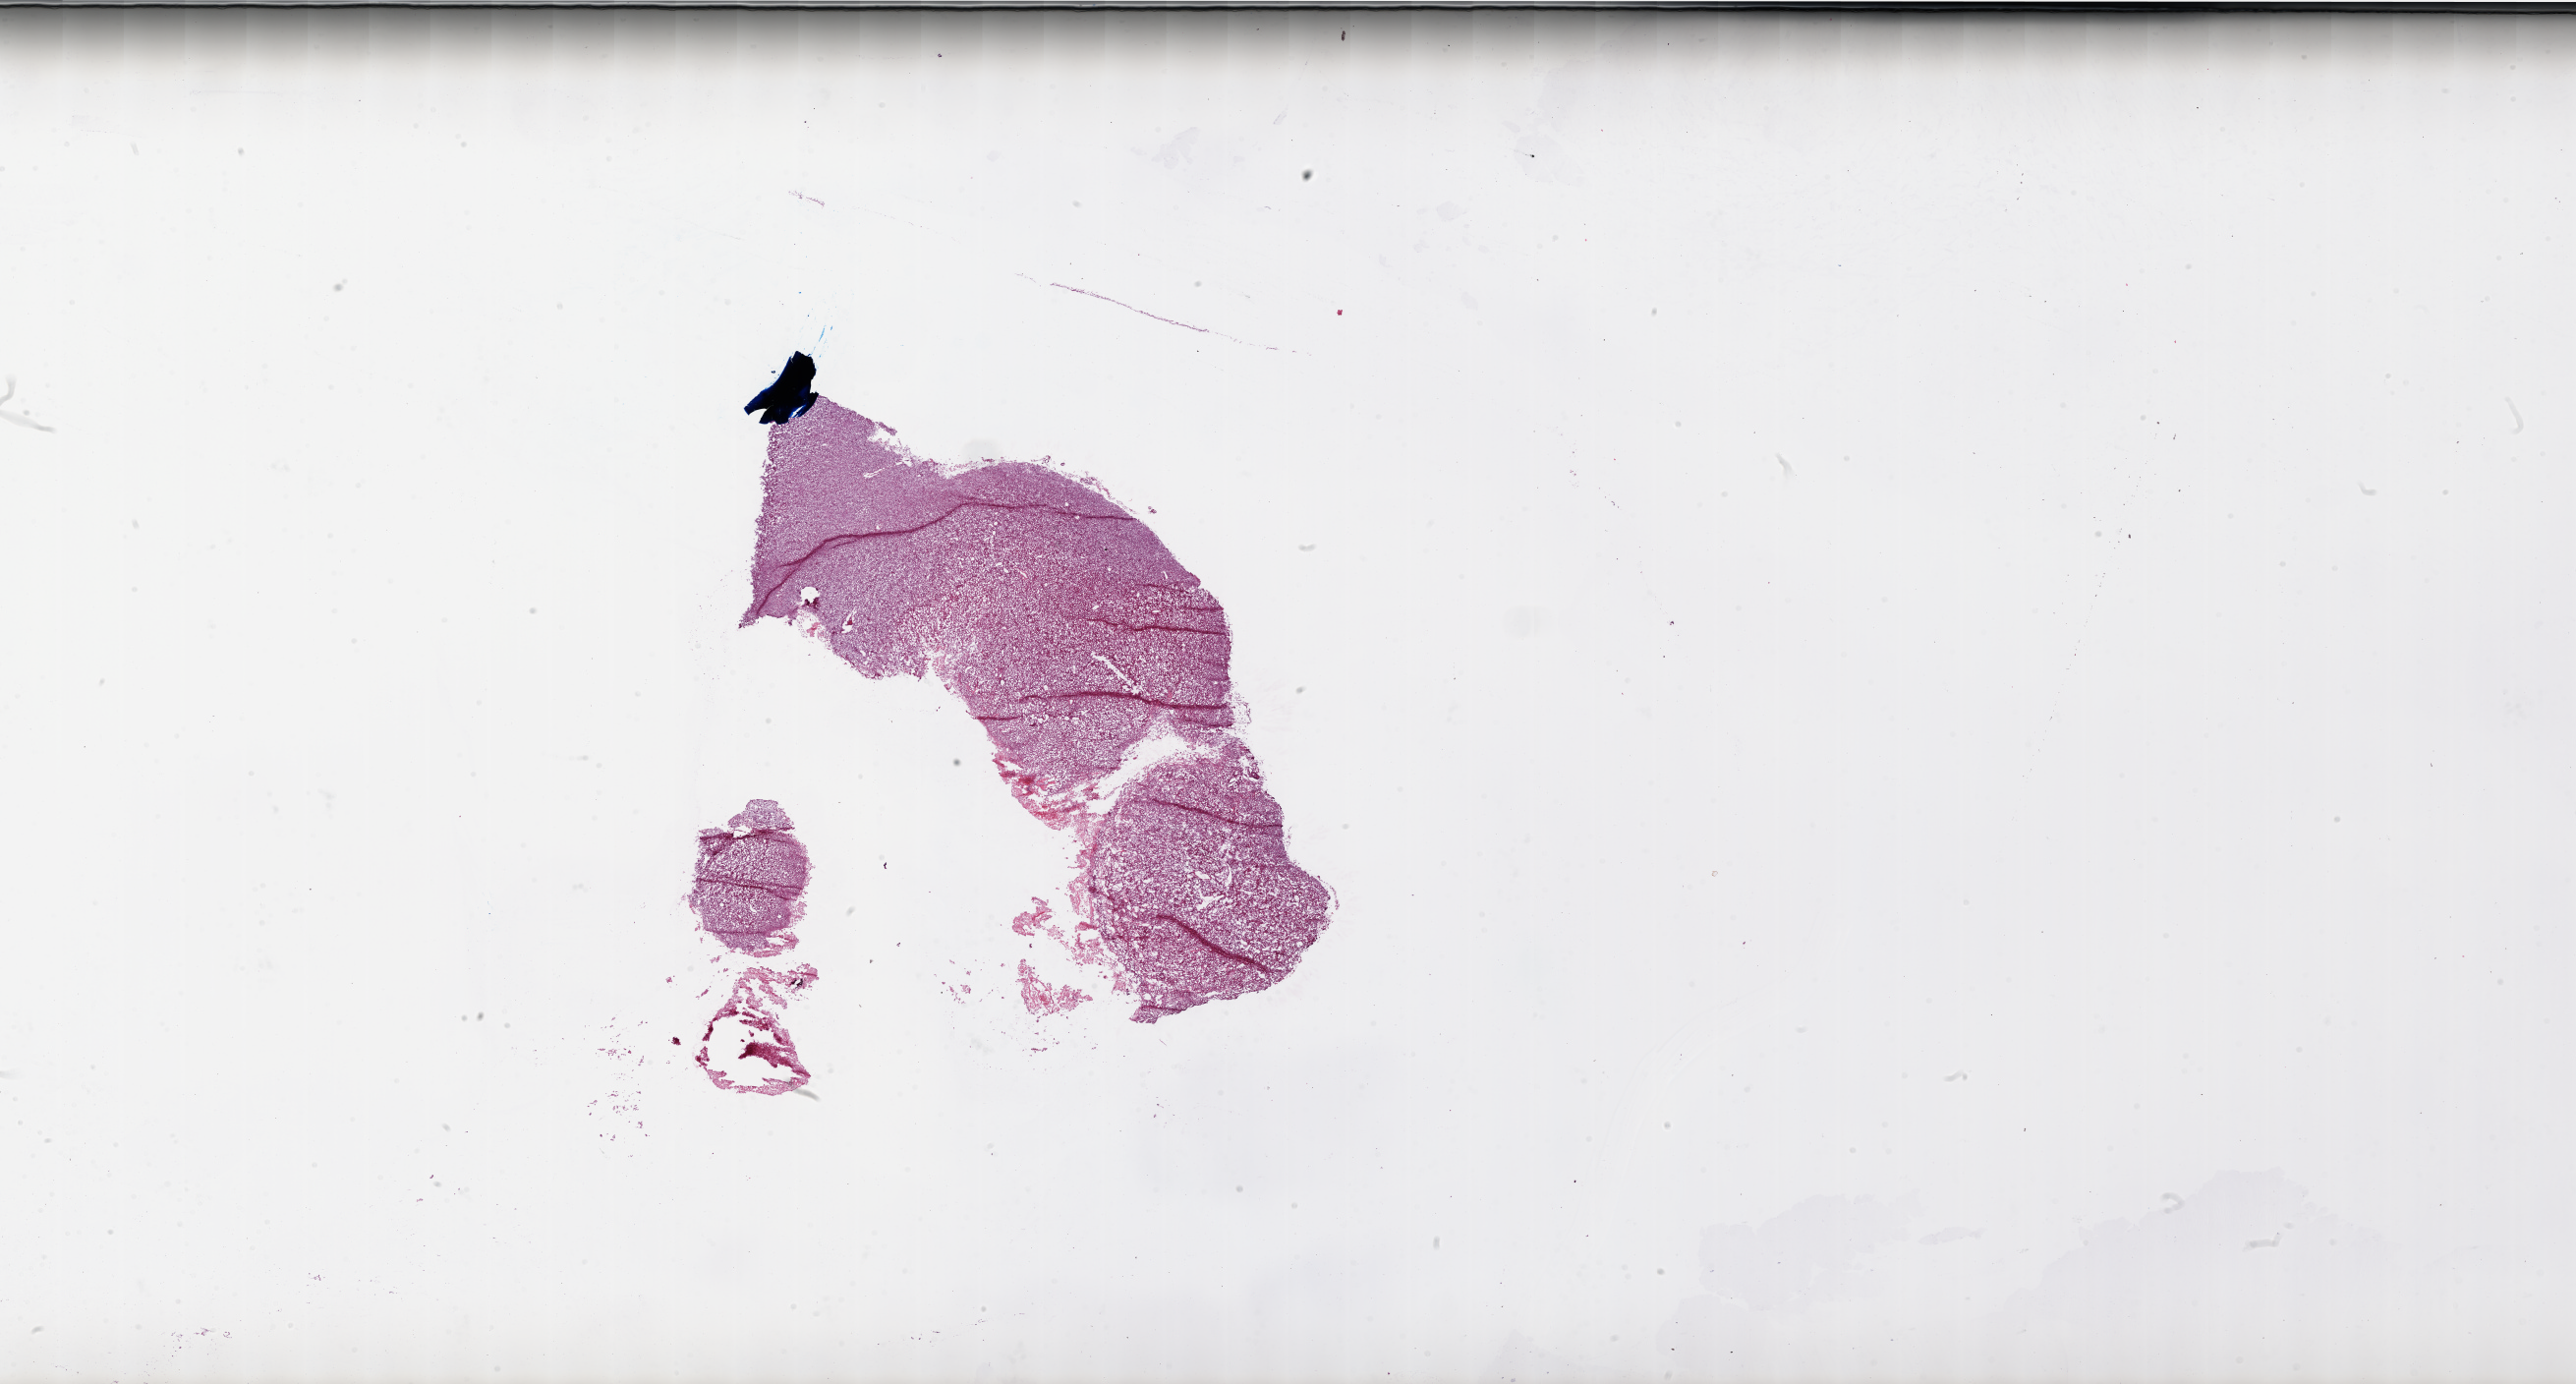
Digitized Hematoxylin and eosin (H&E) stained tissue section (whole slide) — low-resolution overview of the scanned area, about 42.0 x 22.5 mm (acquisition: 20x scan); frozen section from the top of the tissue portion; primary tumour sample from the brain. Male, age 57 years at initial diagnosis.
Pathologic diagnosis: Glioblastoma.